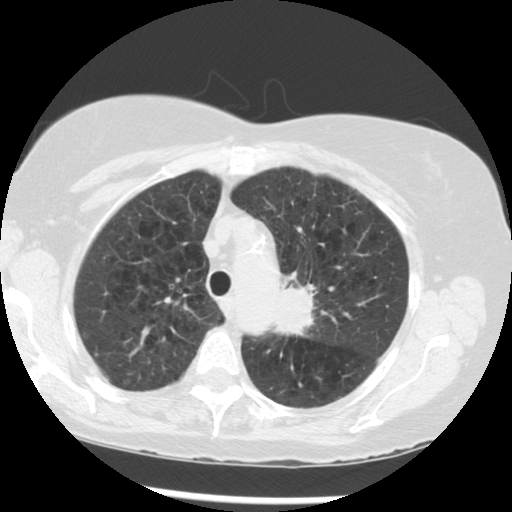
Low-dose screening chest CT, one axial slice. Slice 216 of 283 in the series (ordered by position). Reconstruction kernel STANDARD. Lung window (W 1500 / L -600 HU). 2.5 mm slice thickness. 512 × 512 image matrix, field of view 330 × 330 mm.
Outlined on this slice (manually delineated by an expert):
- lesion 1 (tumor, upper lobe of left lung): box from (x=274, y=276) to (x=313, y=335) px